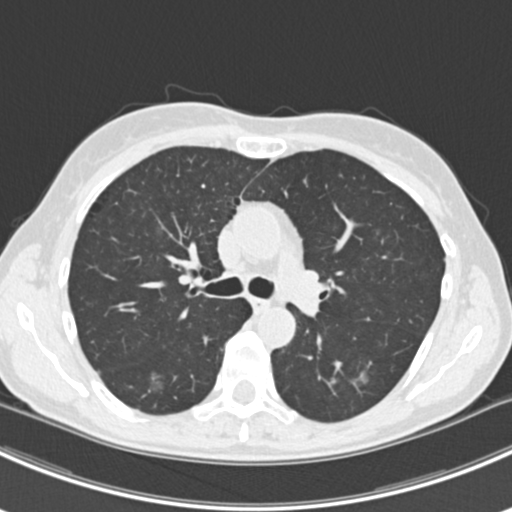
Chest CT (low-dose screening protocol), one axial image; first (baseline) screen; lung window (W 1500 / L -600 HU); 2 mm slice thickness; 120 kVp; slice 67 of 224 in the series. Female participant, aged 63 years at enrolment.
- 2 expert-annotated lung lesions on this slice (largest first), bounding box (x1, y1, x2, y2) in pixels: (135, 364, 179, 403); (344, 362, 384, 394).
- The screening reader recorded 10 non-calcified nodules or masses ≥4 mm on this exam (right lower lobe, right lower lobe, left lower lobe, left lower lobe, right middle lobe, right lower lobe, left lower lobe, left upper lobe, right upper lobe, left upper lobe); which of them these boxes mark is not recorded.
- Lung cancer was diagnosed 751 days after this screen (after the third annual screen): bronchiolo-alveolar adenocarcinoma, NOS, right upper lobe, right middle lobe, right lower lobe, left upper lobe, left lower lobe, moderately differentiated (G2), stage IV (AJCC 6th edition).